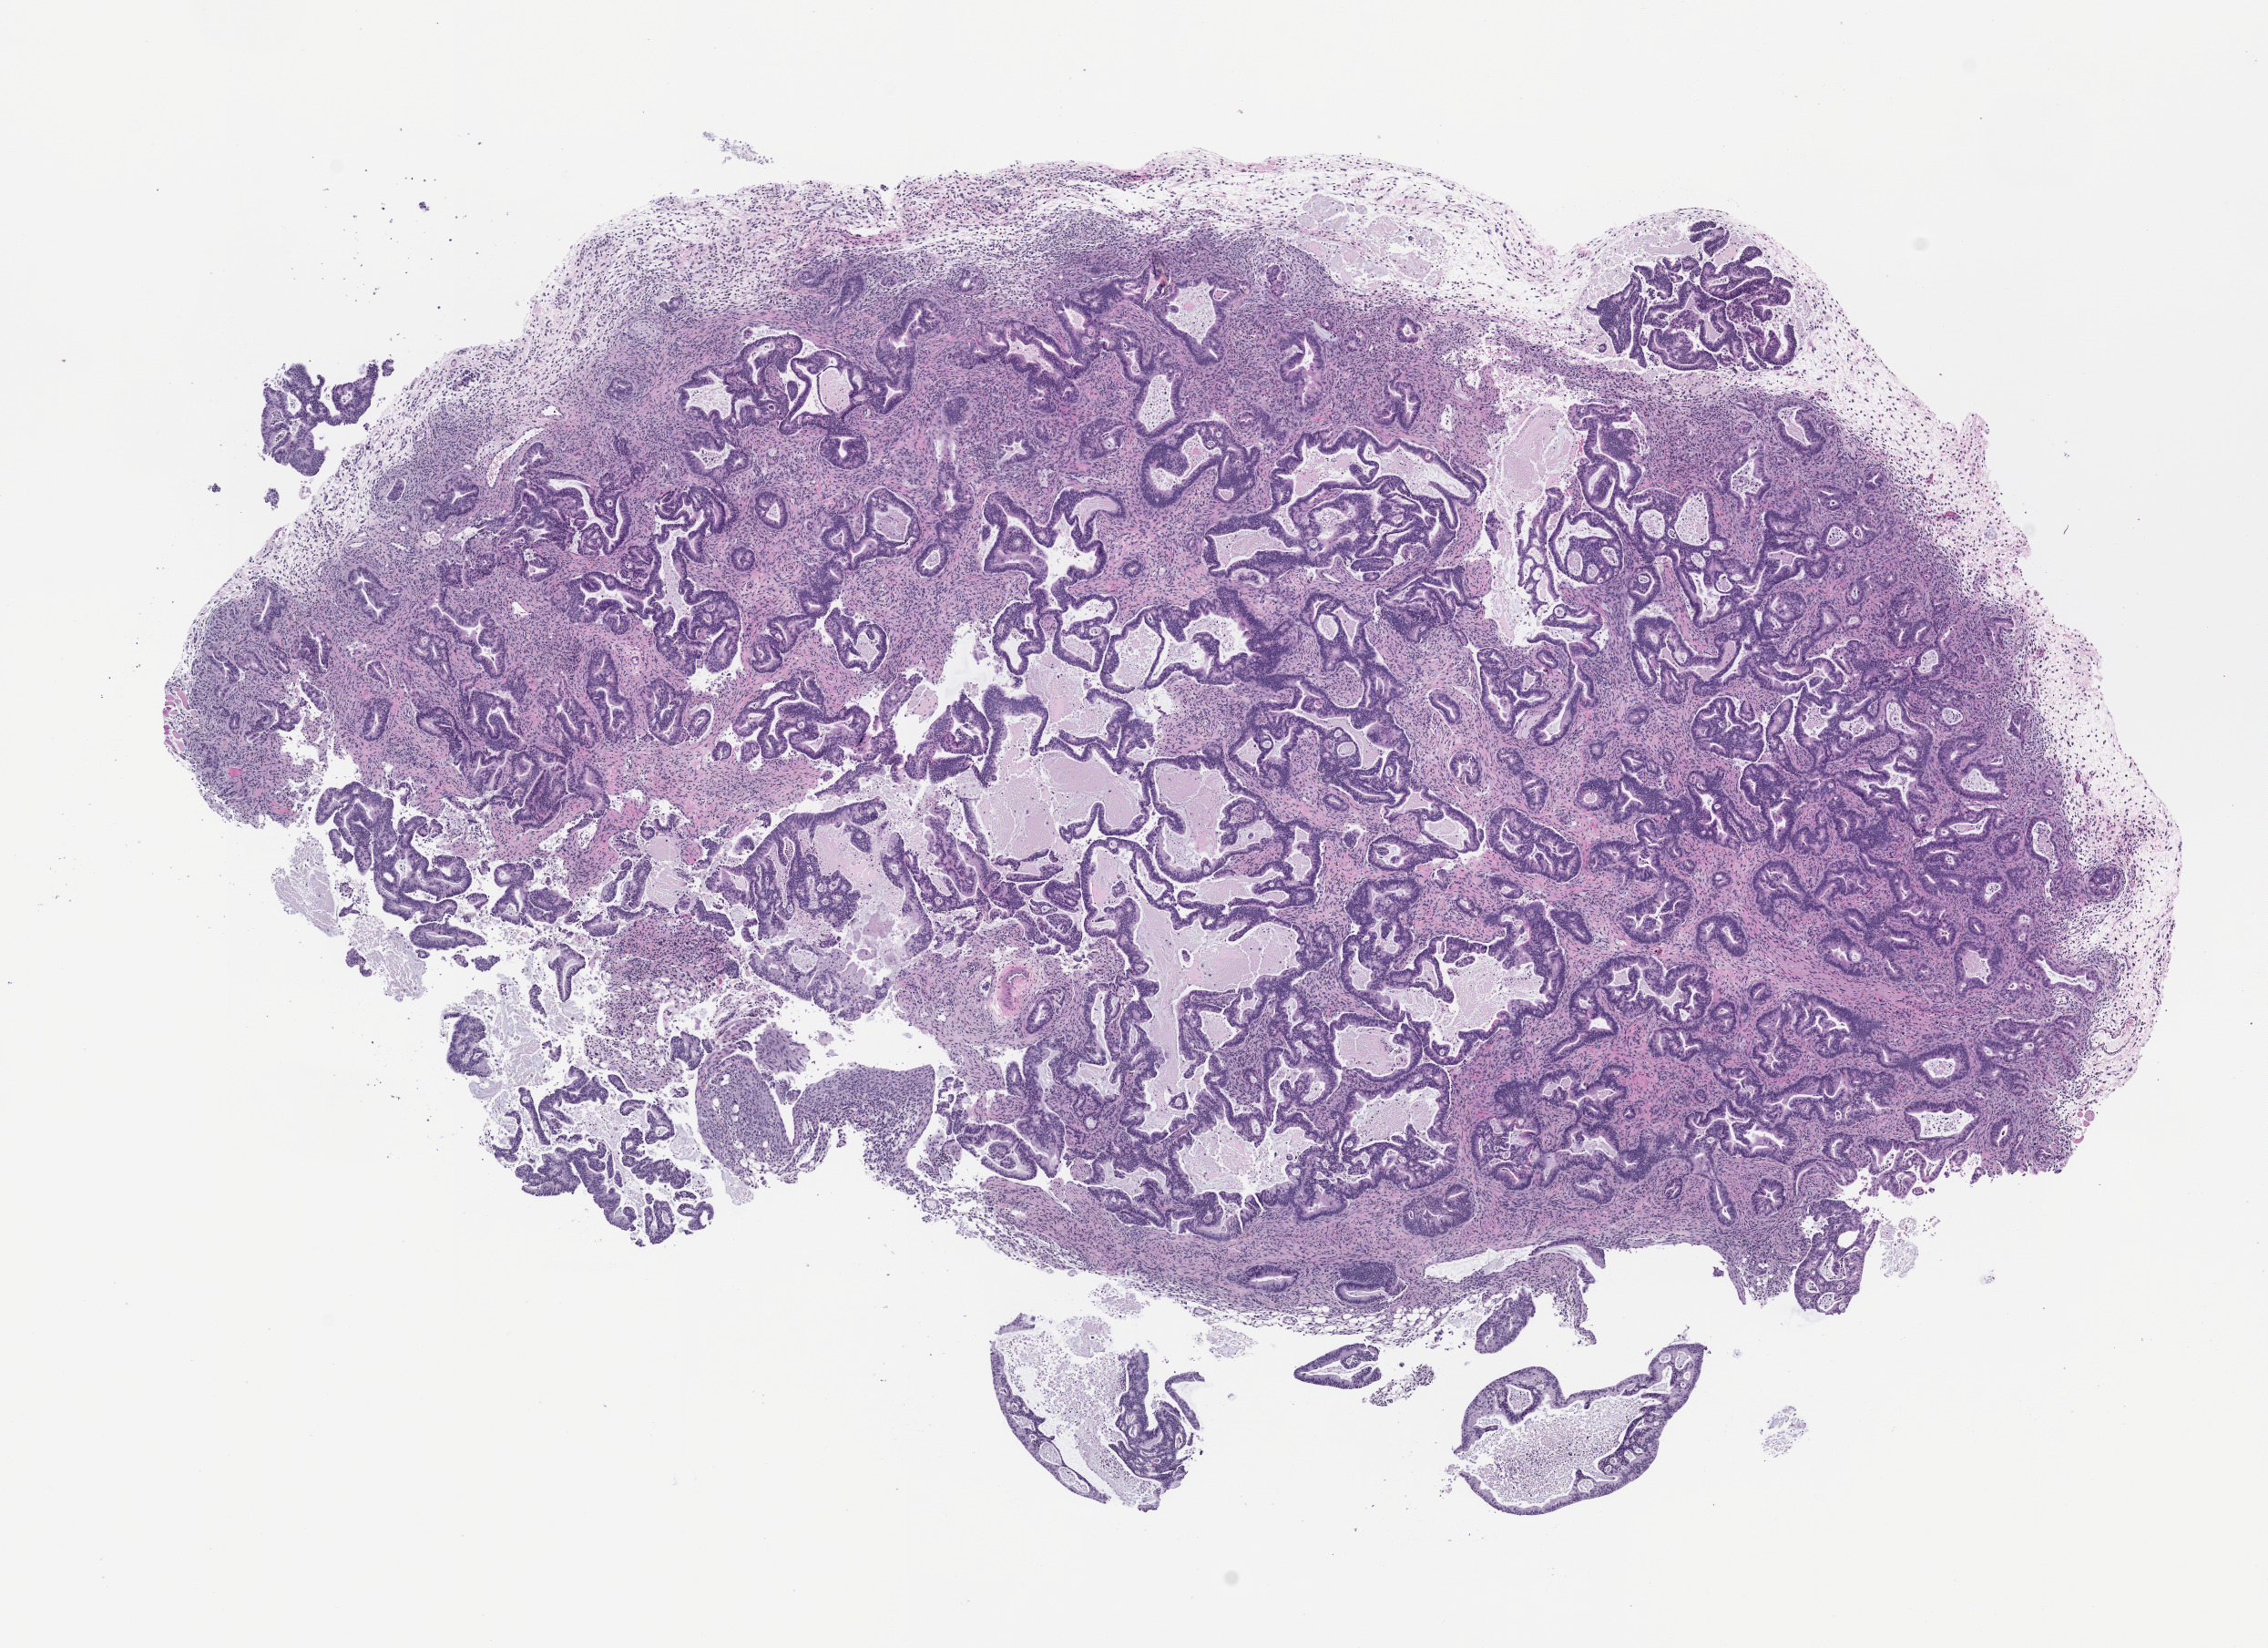
H&E whole-slide image of a patient-derived xenograft (PDX) tumor grown in a mouse, passage 2 — whole scanned area (about 10.0 x 7.3 mm) shown as a low-resolution overview. FFPE section. Tumor site category: pancreas.
• originating patient diagnosis: Pancreatic Adenocarcinoma